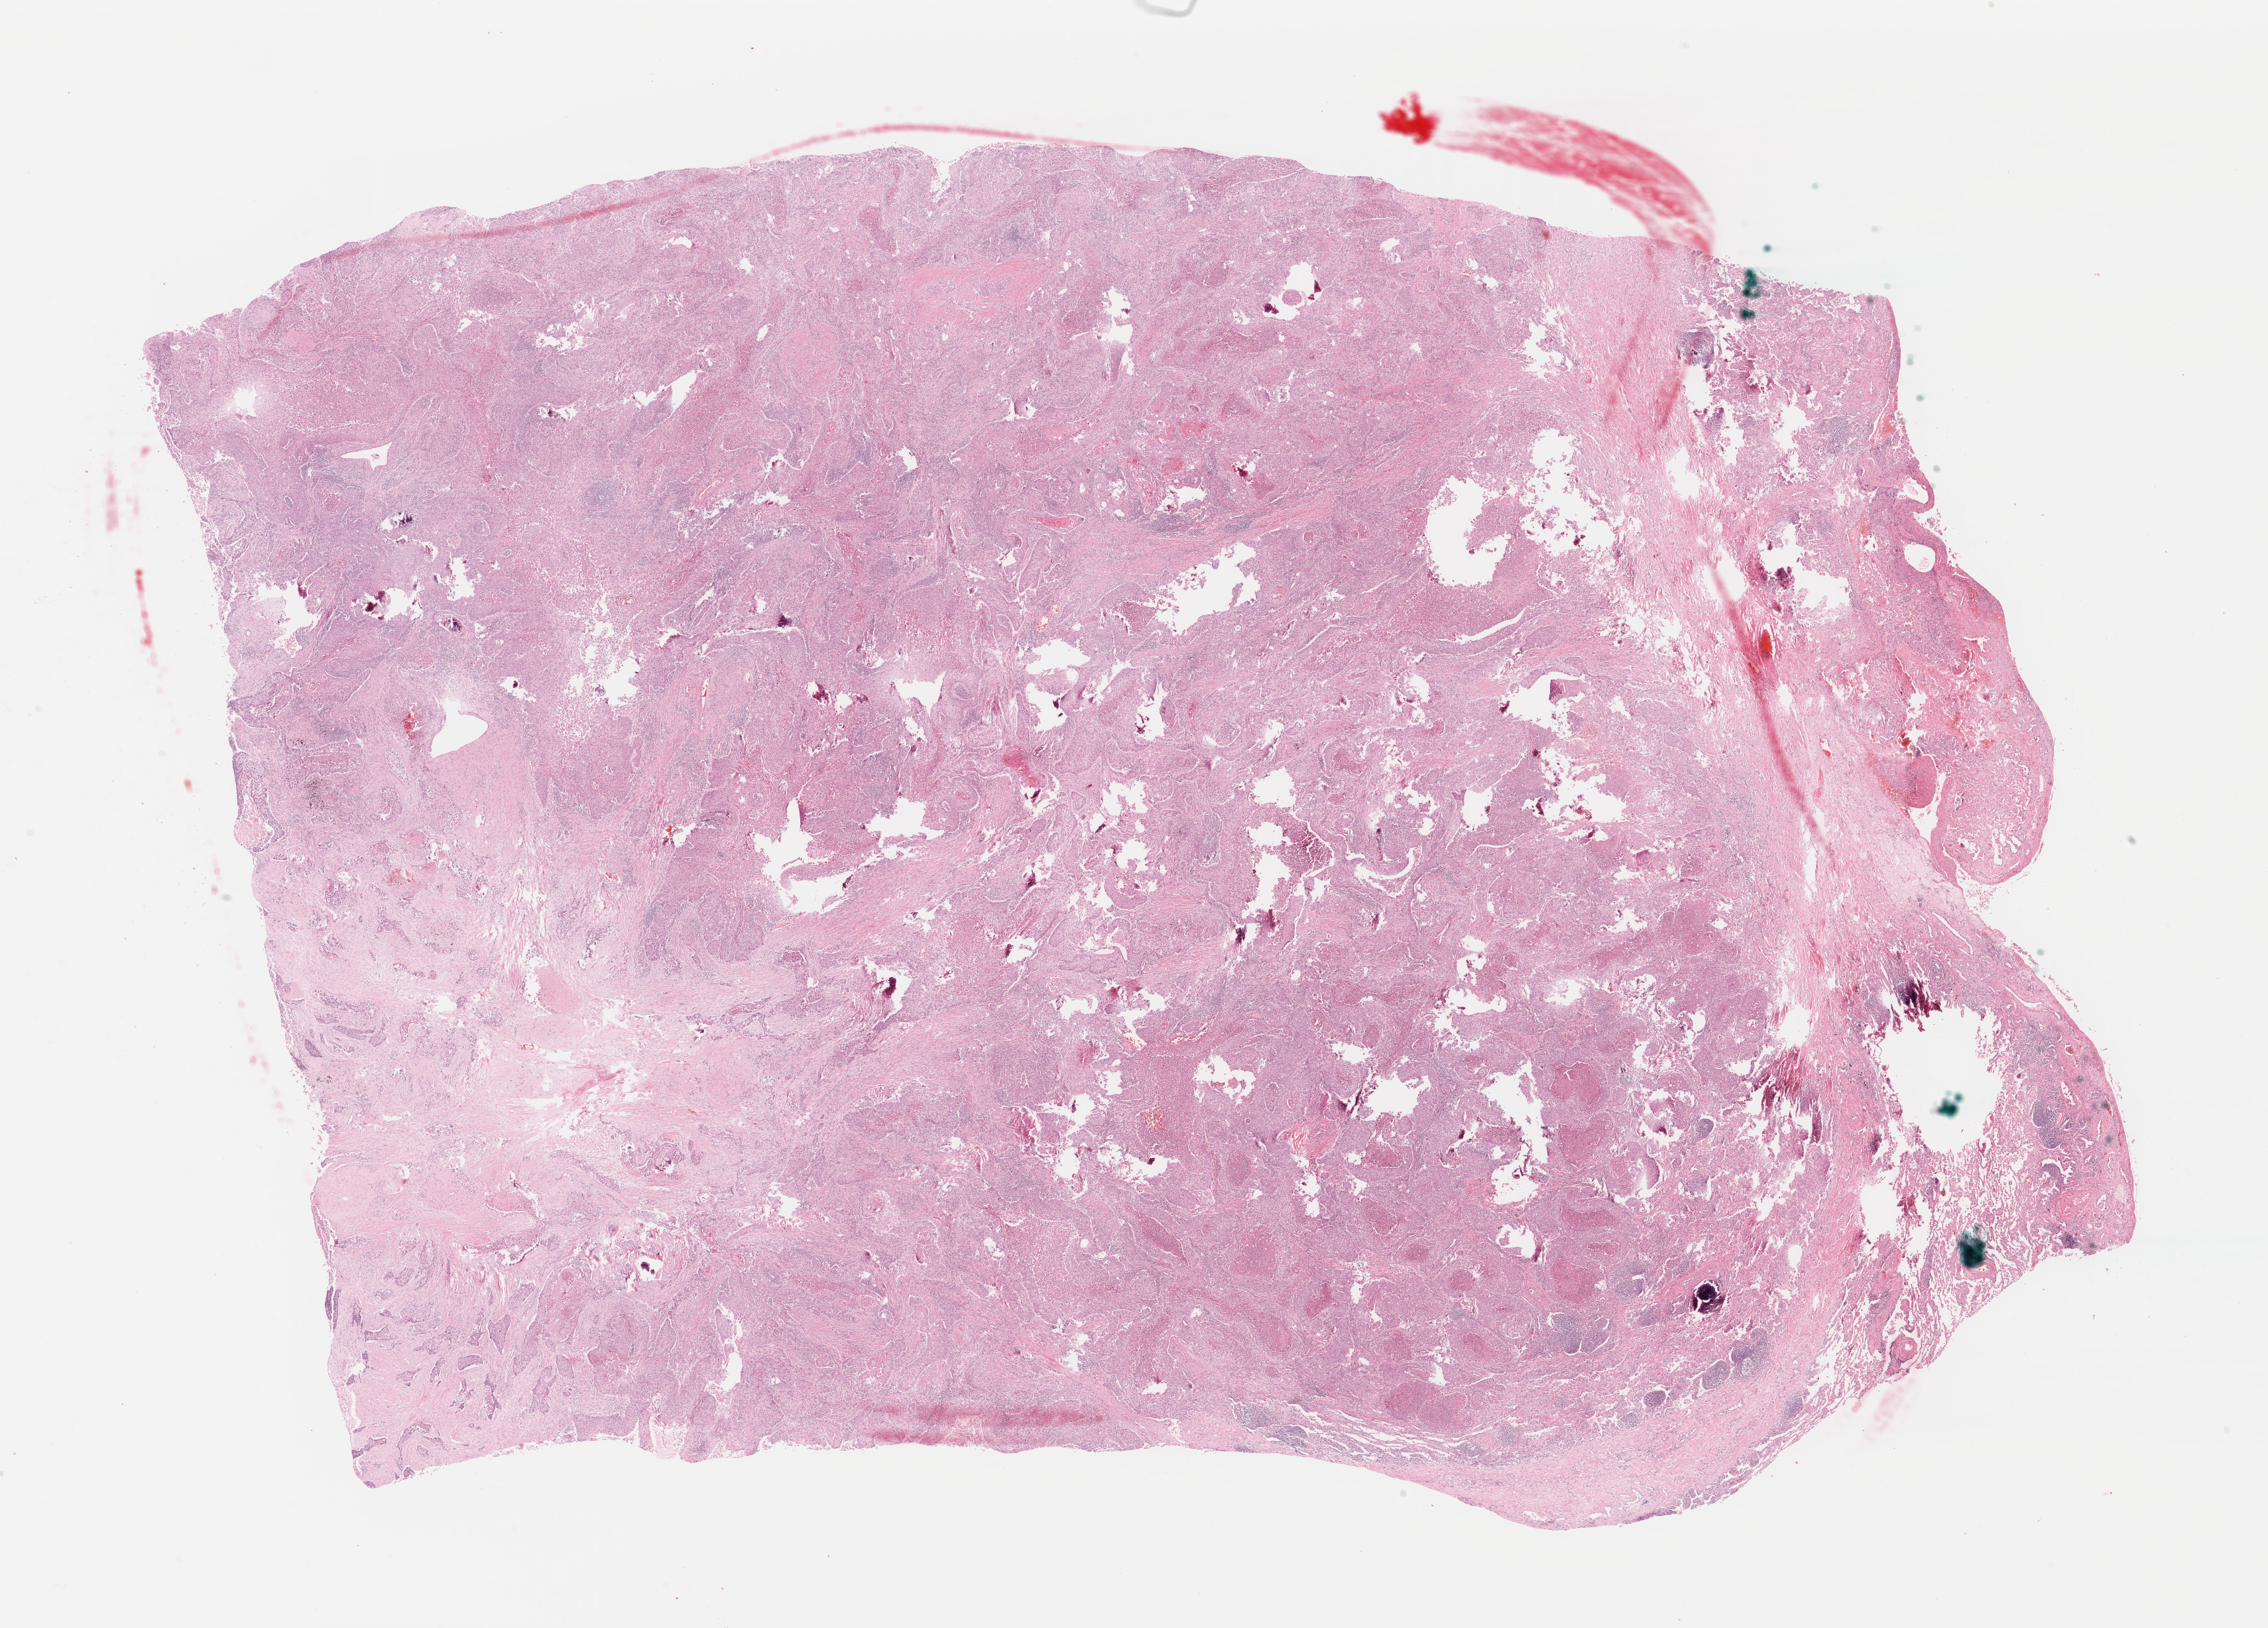
Whole-slide histology image, H&E-stained, low-resolution overview of the scanned area, about 26.9 x 19.3 mm (acquisition: 40x scan). Formalin-fixed paraffin-embedded (FFPE) diagnostic section. Primary tumour sample from the lung. Male patient; age at initial diagnosis 62 years.
Histologic diagnosis: Squamous cell carcinoma, NOS (lower lobe, lung). AJCC pathologic stage: IIB.